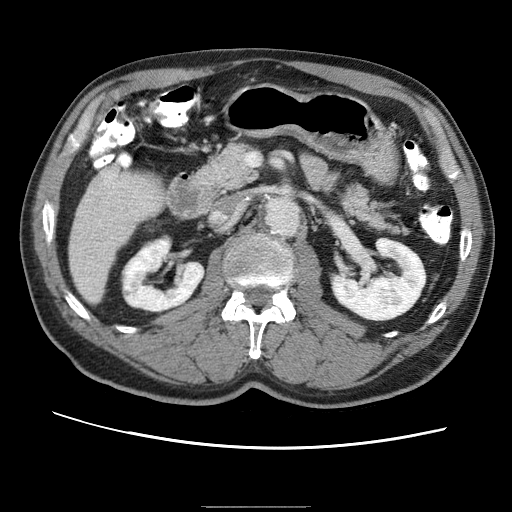
Contrast-enhanced abdominal CT (liver protocol), one axial slice; slice 13 of 75 in the series (ordered by position); reconstruction kernel STANDARD; one of 2 acquisitions stored at this slice position; soft-tissue window (W 400 / L 40 HU); 2.5 mm slice thickness; 512 × 512 image matrix, field of view 360 × 360 mm. From the clinical record (not read from this slice): diagnosis: hepatocellular carcinoma (patient treated with transarterial chemoembolisation; whether this scan precedes or follows treatment is not stated here); TNM stage (as recorded): Stage-II; Child-Pugh class: A; tumour differentiation: well differentiated.
Annotated regions visible in this slice (semi-automatically segmented with operator editing):
- liver parenchyma outside the tumour (the mass and vessels are separate outlines, so this box may not span the whole liver): bounding box <70,167,126,296> (left, top, right, bottom; pixels)
- liver vessels: <76,169,122,257>